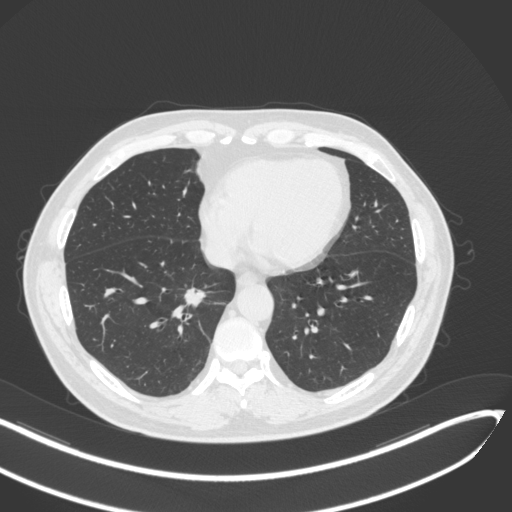
Chest CT, one axial slice. 120 kVp. Lung window (W 1500 / L -600 HU). 1 mm slice thickness. 512 × 512 image matrix. Male patient, age 62 years. Case-level facts recorded for this patient, not image findings: clinical TNM (as recorded): T1b N0 M0; histopathological grade: G2.
Outlined on this slice (bounding box drawn by a radiologist):
- lung tumour (recorded histology: adenocarcinoma): bounding box [x1, y1, x2, y2] px = [182, 285, 215, 307]